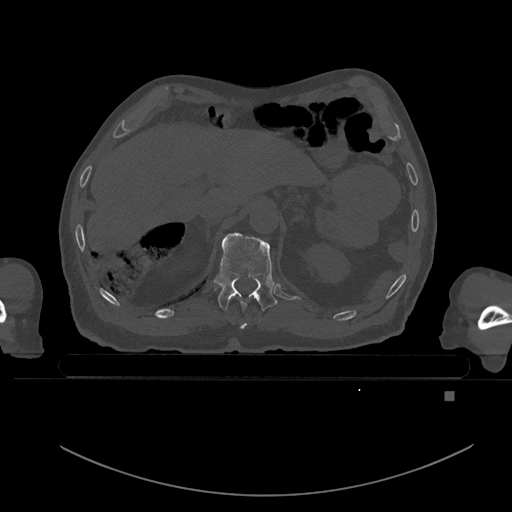
CT including the spine, one axial slice. Position 38 of 969 along the scan axis. Bone window (W 1800 / L 400 HU). 0.5 mm slice thickness. 512 × 512 image matrix. Male patient, age 82 years. From the clinical record (not read from this slice): primary cancer: prostate; vertebrae with lytic lesions (as recorded): T11, T9, T8, T2.
Annotated regions visible in this slice (semi-automatic segmentation, software-assisted and operator-edited):
- T10 vertebra: box from (x=239, y=322) to (x=247, y=329) px
- T11 vertebra: (x=214, y=232)–(x=277, y=311)